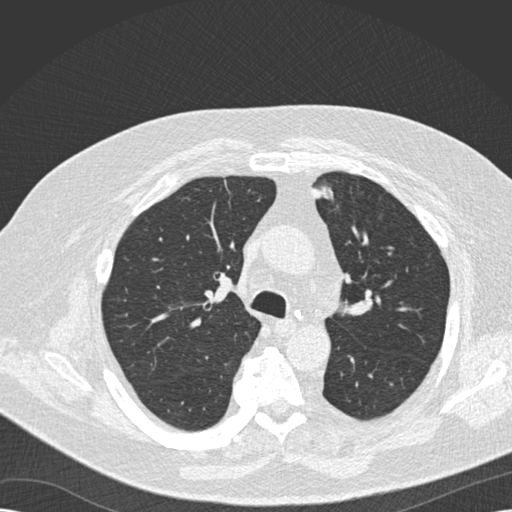
Low-dose screening chest CT, one axial slice; position 114 of 173 along the scan axis; reconstruction kernel B30f; 120 kVp; lung window (W 1500 / L -600 HU); 2 mm slice thickness; 512 × 512 image matrix.
Structures marked on this image (outlined manually by an expert reader):
- lesion 1 (tumor, upper lobe of left lung): box from (x=313, y=185) to (x=333, y=198) px